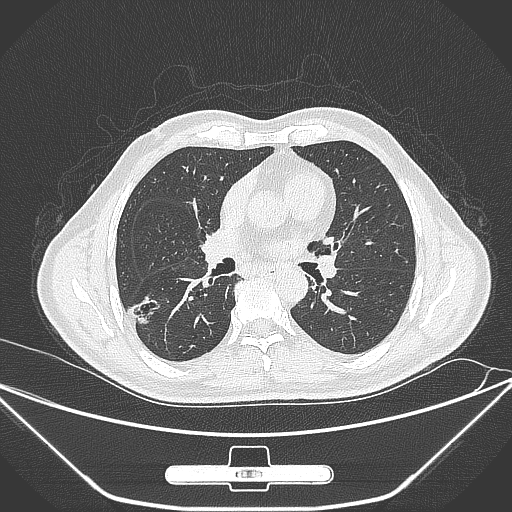
Chest CT, one axial slice; position 152 of 310 along the scan axis; 120 kVp; lung window (W 1500 / L -600 HU); 512 × 512 image matrix, field of view 398 × 398 mm. Male patient, age 71 years. Case-level facts recorded for this patient, not image findings: clinical TNM (as recorded): T1c N0 M0.
Annotated regions visible in this slice (rectangle marked by the reading radiologist):
- lung tumour (recorded histology: adenocarcinoma): bounding box (x1, y1, x2, y2) in pixels: (125, 296, 169, 336)